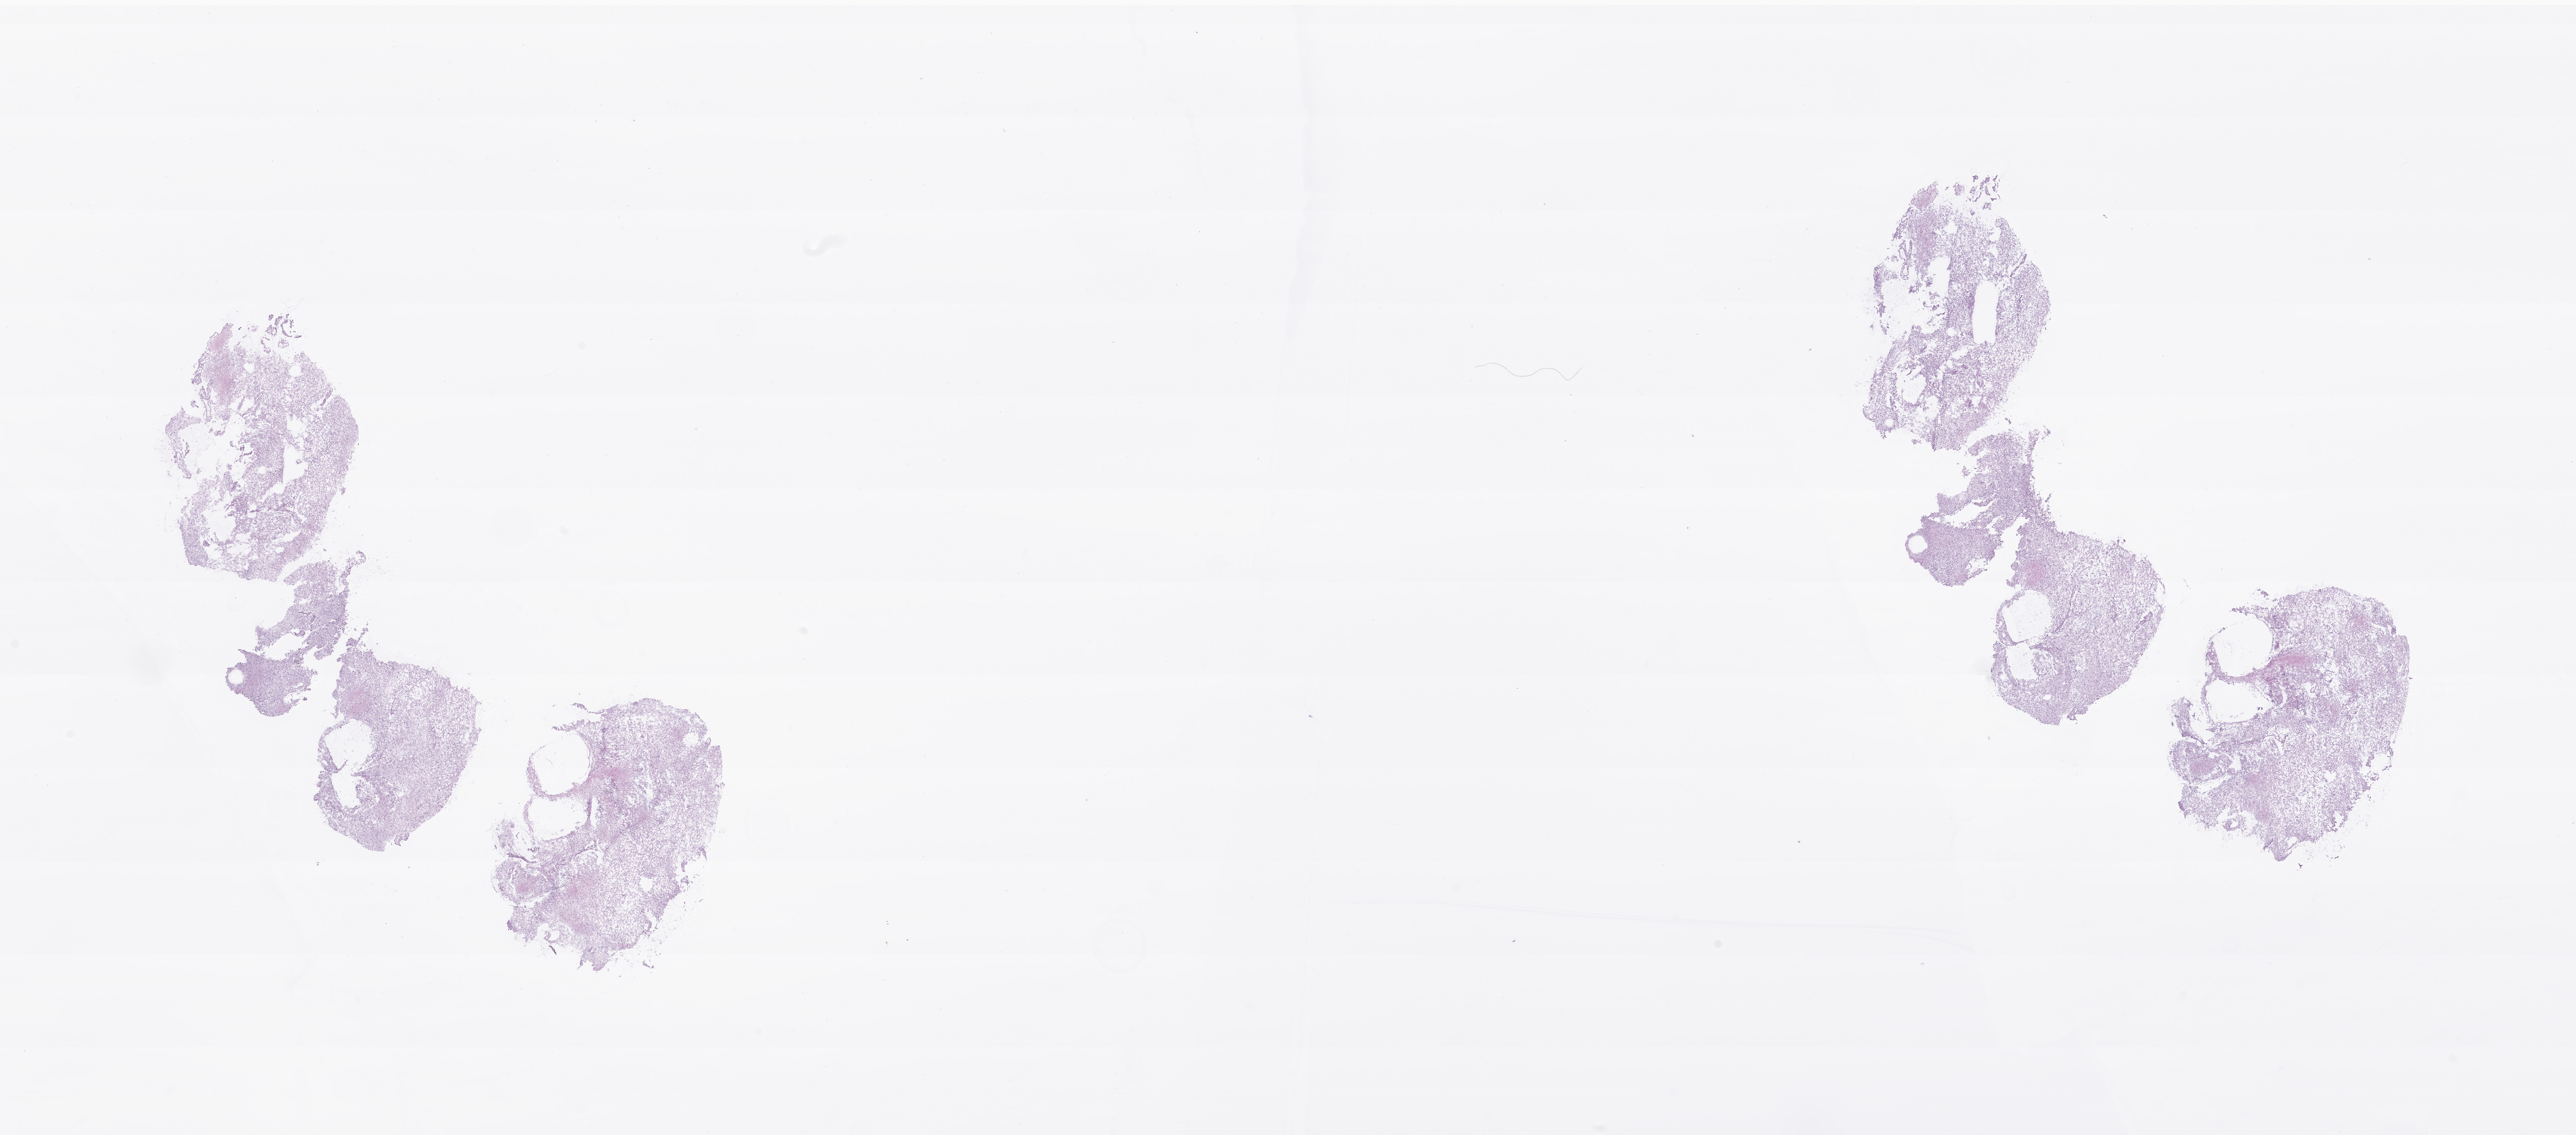
Digitized hematoxylin and eosin (H&E)-stained section of tumor tissue from the brain — a low-resolution overview of the entire scanned area, about 29.5 x 13.0 mm. Cryosection (OCT / tissue freezing medium). Patient male; age 58 months (4 years 10 months).
Recorded diagnosis: Tumor cells, uncertain whether benign or malignant.